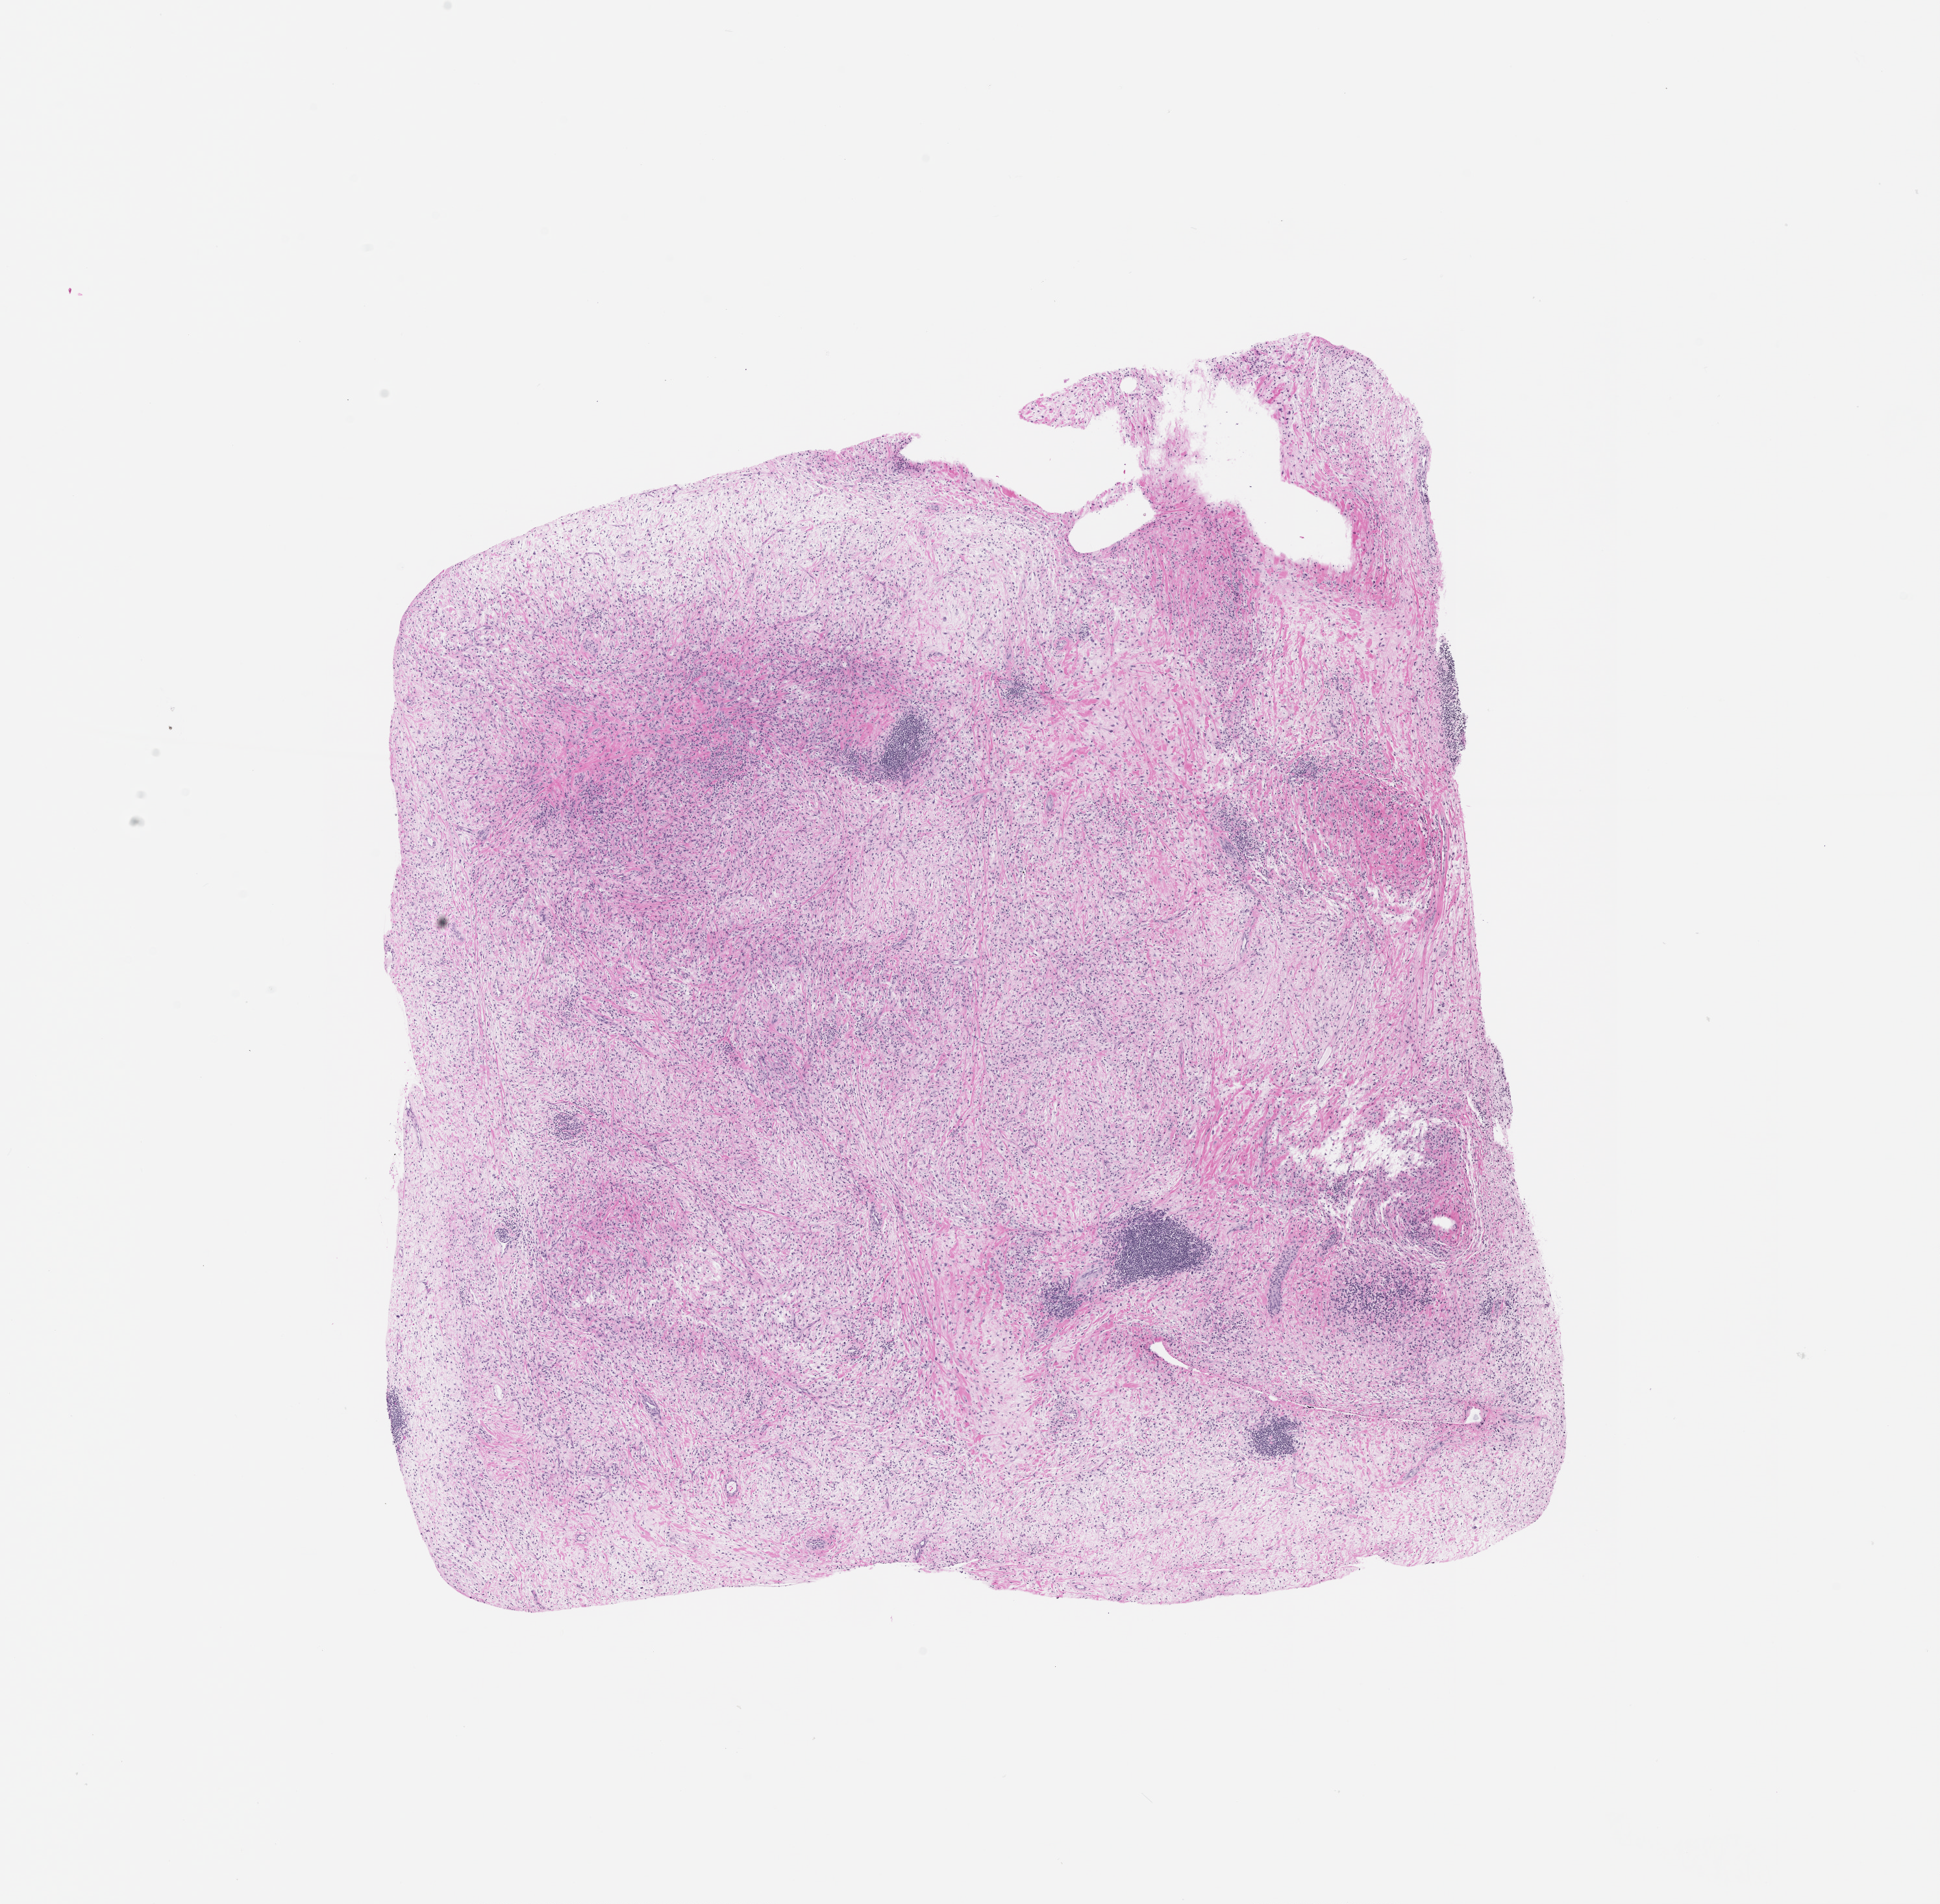
Digitized H&E tissue section (whole slide), shown as a low-resolution overview of the whole scanned area (about 12.0 x 11.8 mm).
Patient diagnosis (cohort enrolment): sarcoma (site not recorded at cohort level).